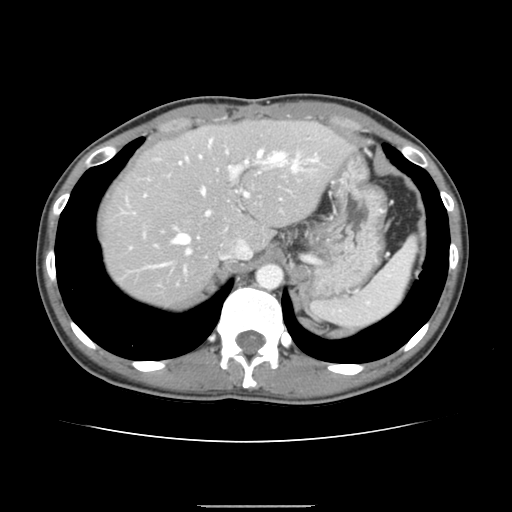
Contrast-enhanced abdominal CT, one axial slice. Position 113 of 150 along the scan axis. 120 kVp. Intravenous contrast given. Soft-tissue window (W 400 / L 40 HU). 512 × 512 image matrix, field of view 324 × 324 mm. Female patient, age 32 years. From the clinical record (not read from this slice): diagnosis: colorectal cancer liver metastases, imaged before liver resection; multiple liver metastases: yes; largest metastasis: 0.7 cm; disease in both lobes: no.
Outlined on this slice (outlined manually by an expert reader):
- hepatic veins: bounding box (x1, y1, x2, y2) in pixels: (145, 150, 297, 273)
- liver: (102, 121, 348, 307)
- planned liver remnant (the part of the liver to remain after resection): (102, 121, 349, 268)
- portal vein (with intrahepatic branches): (145, 139, 318, 215)